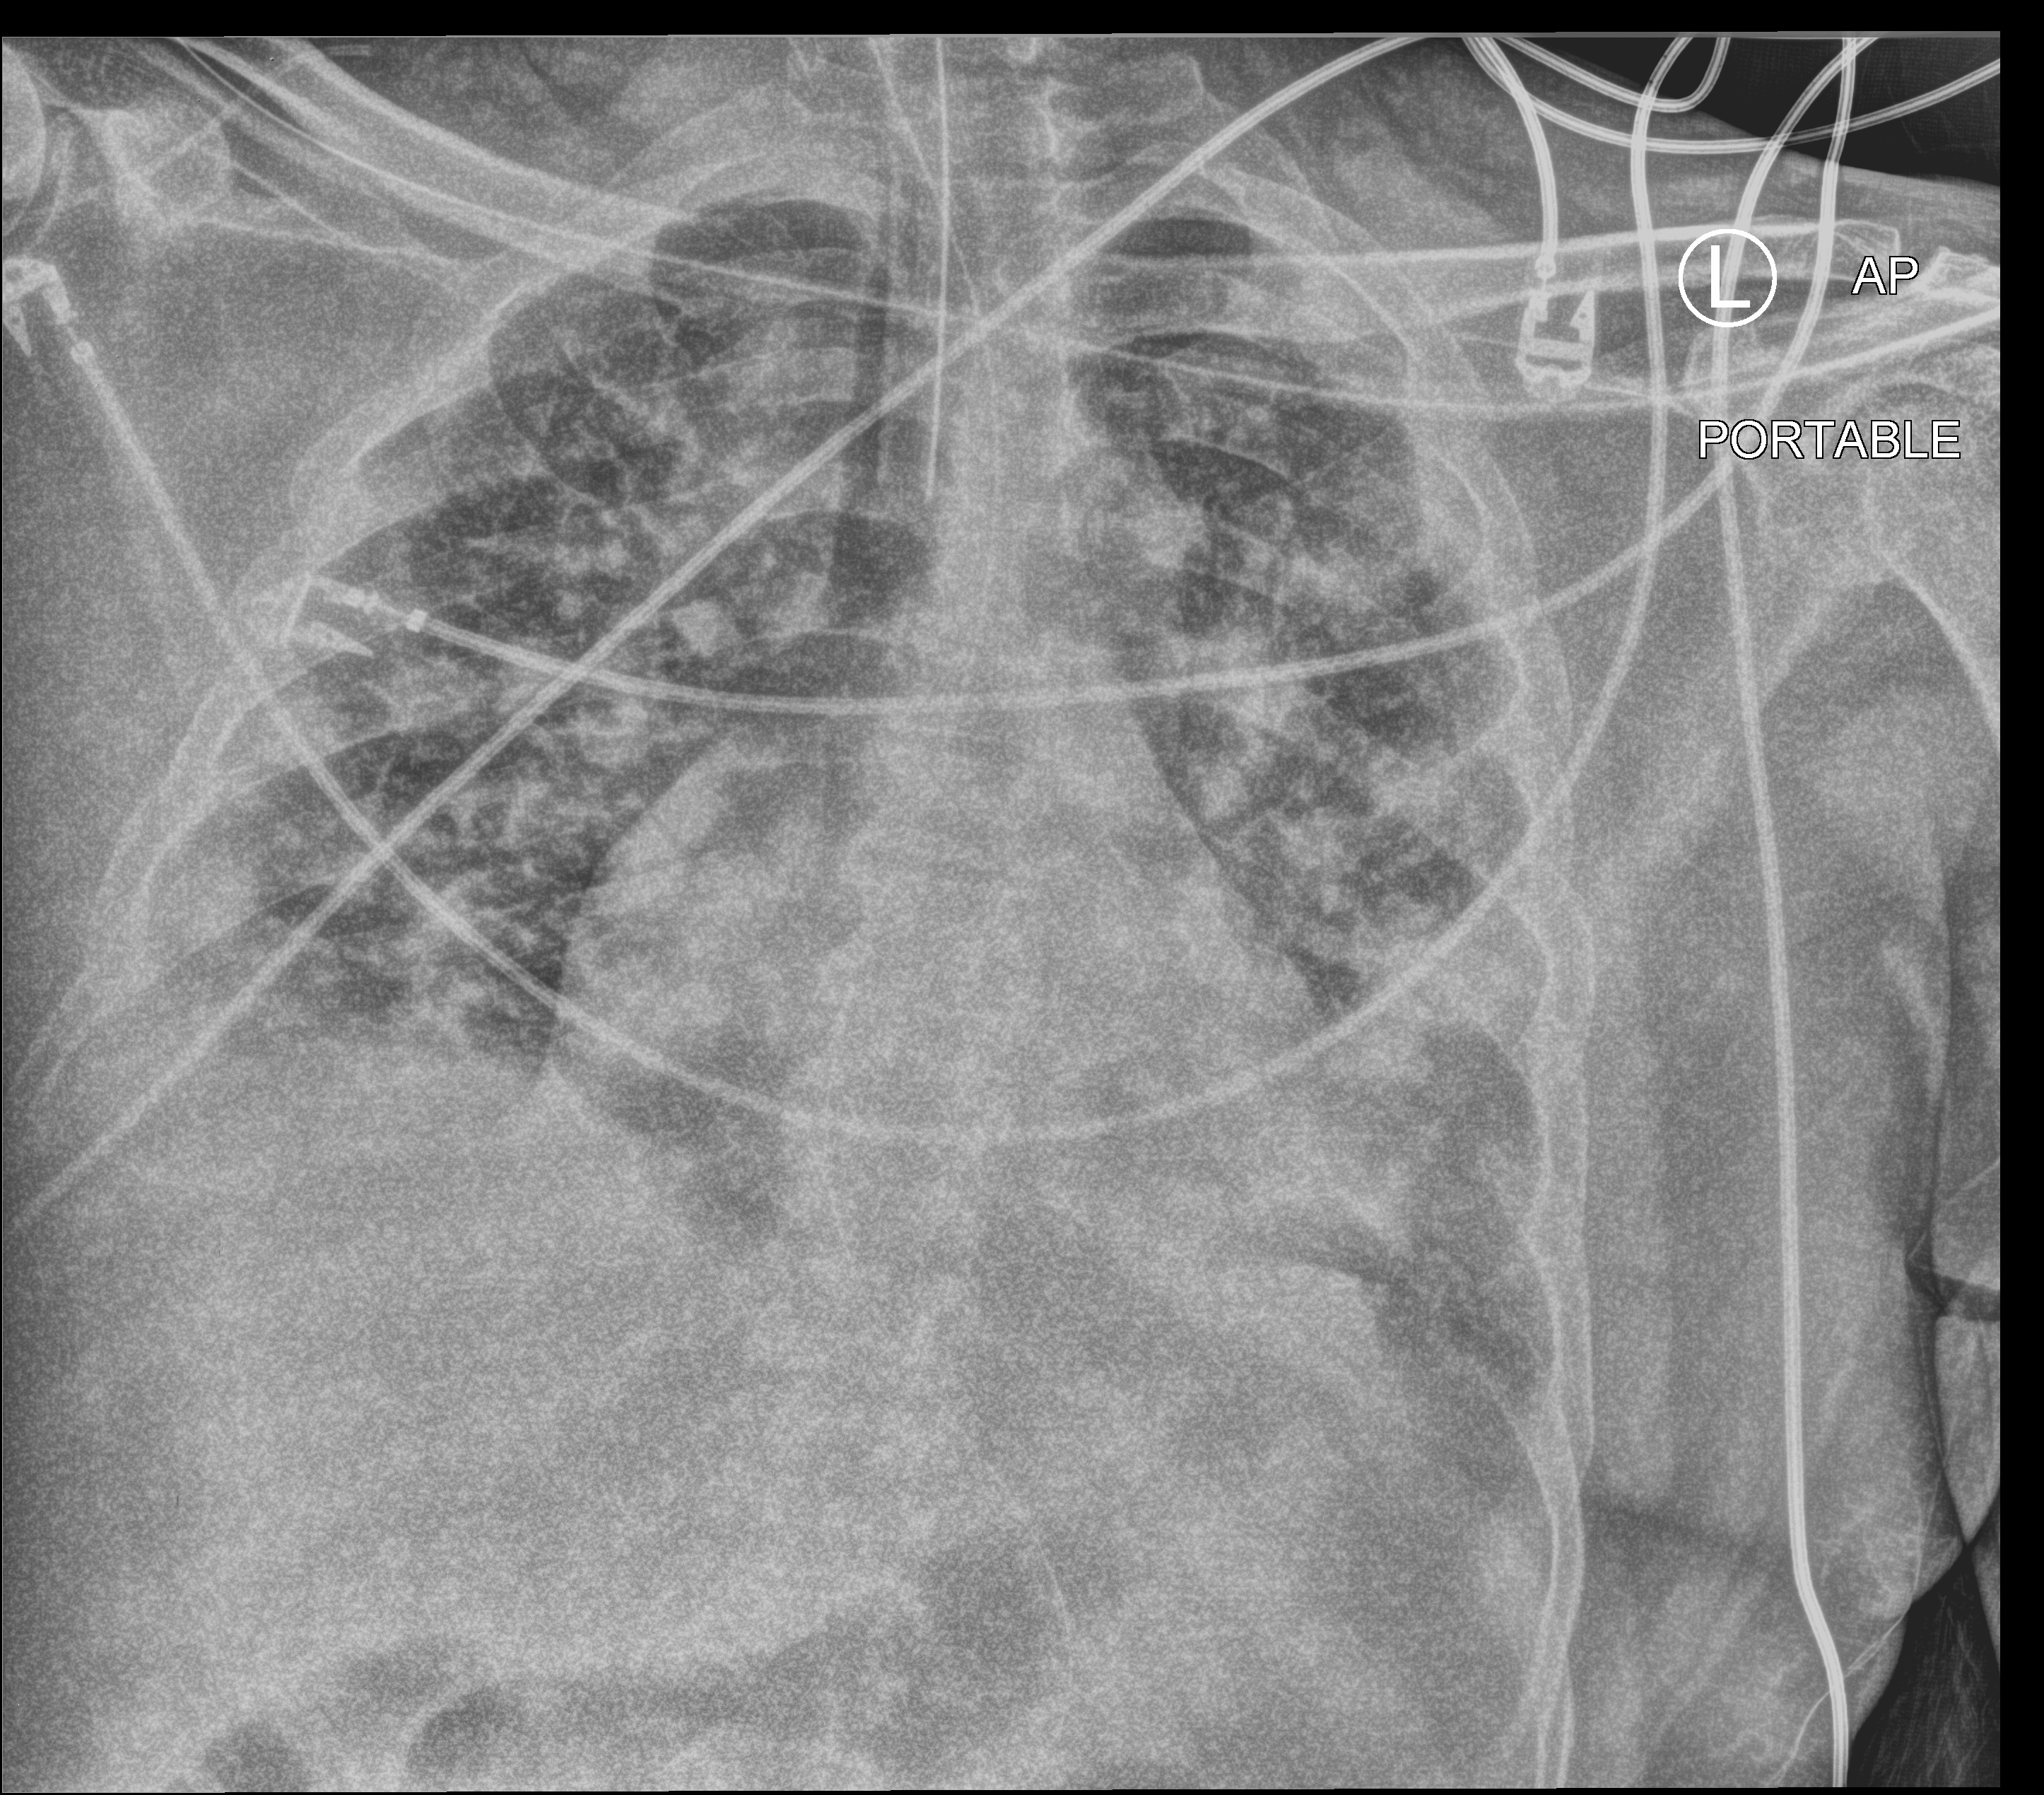
Bedside chest radiograph (computed radiography). Patient hospitalised with COVID-19; male, aged 18–59 years.
Admission-level facts for this patient (not findings on this image; timing relative to this image not recorded): admitted to intensive care during this hospital stay: yes; other chronic lung disease (admission record): yes; mechanically ventilated during this hospital stay: yes.